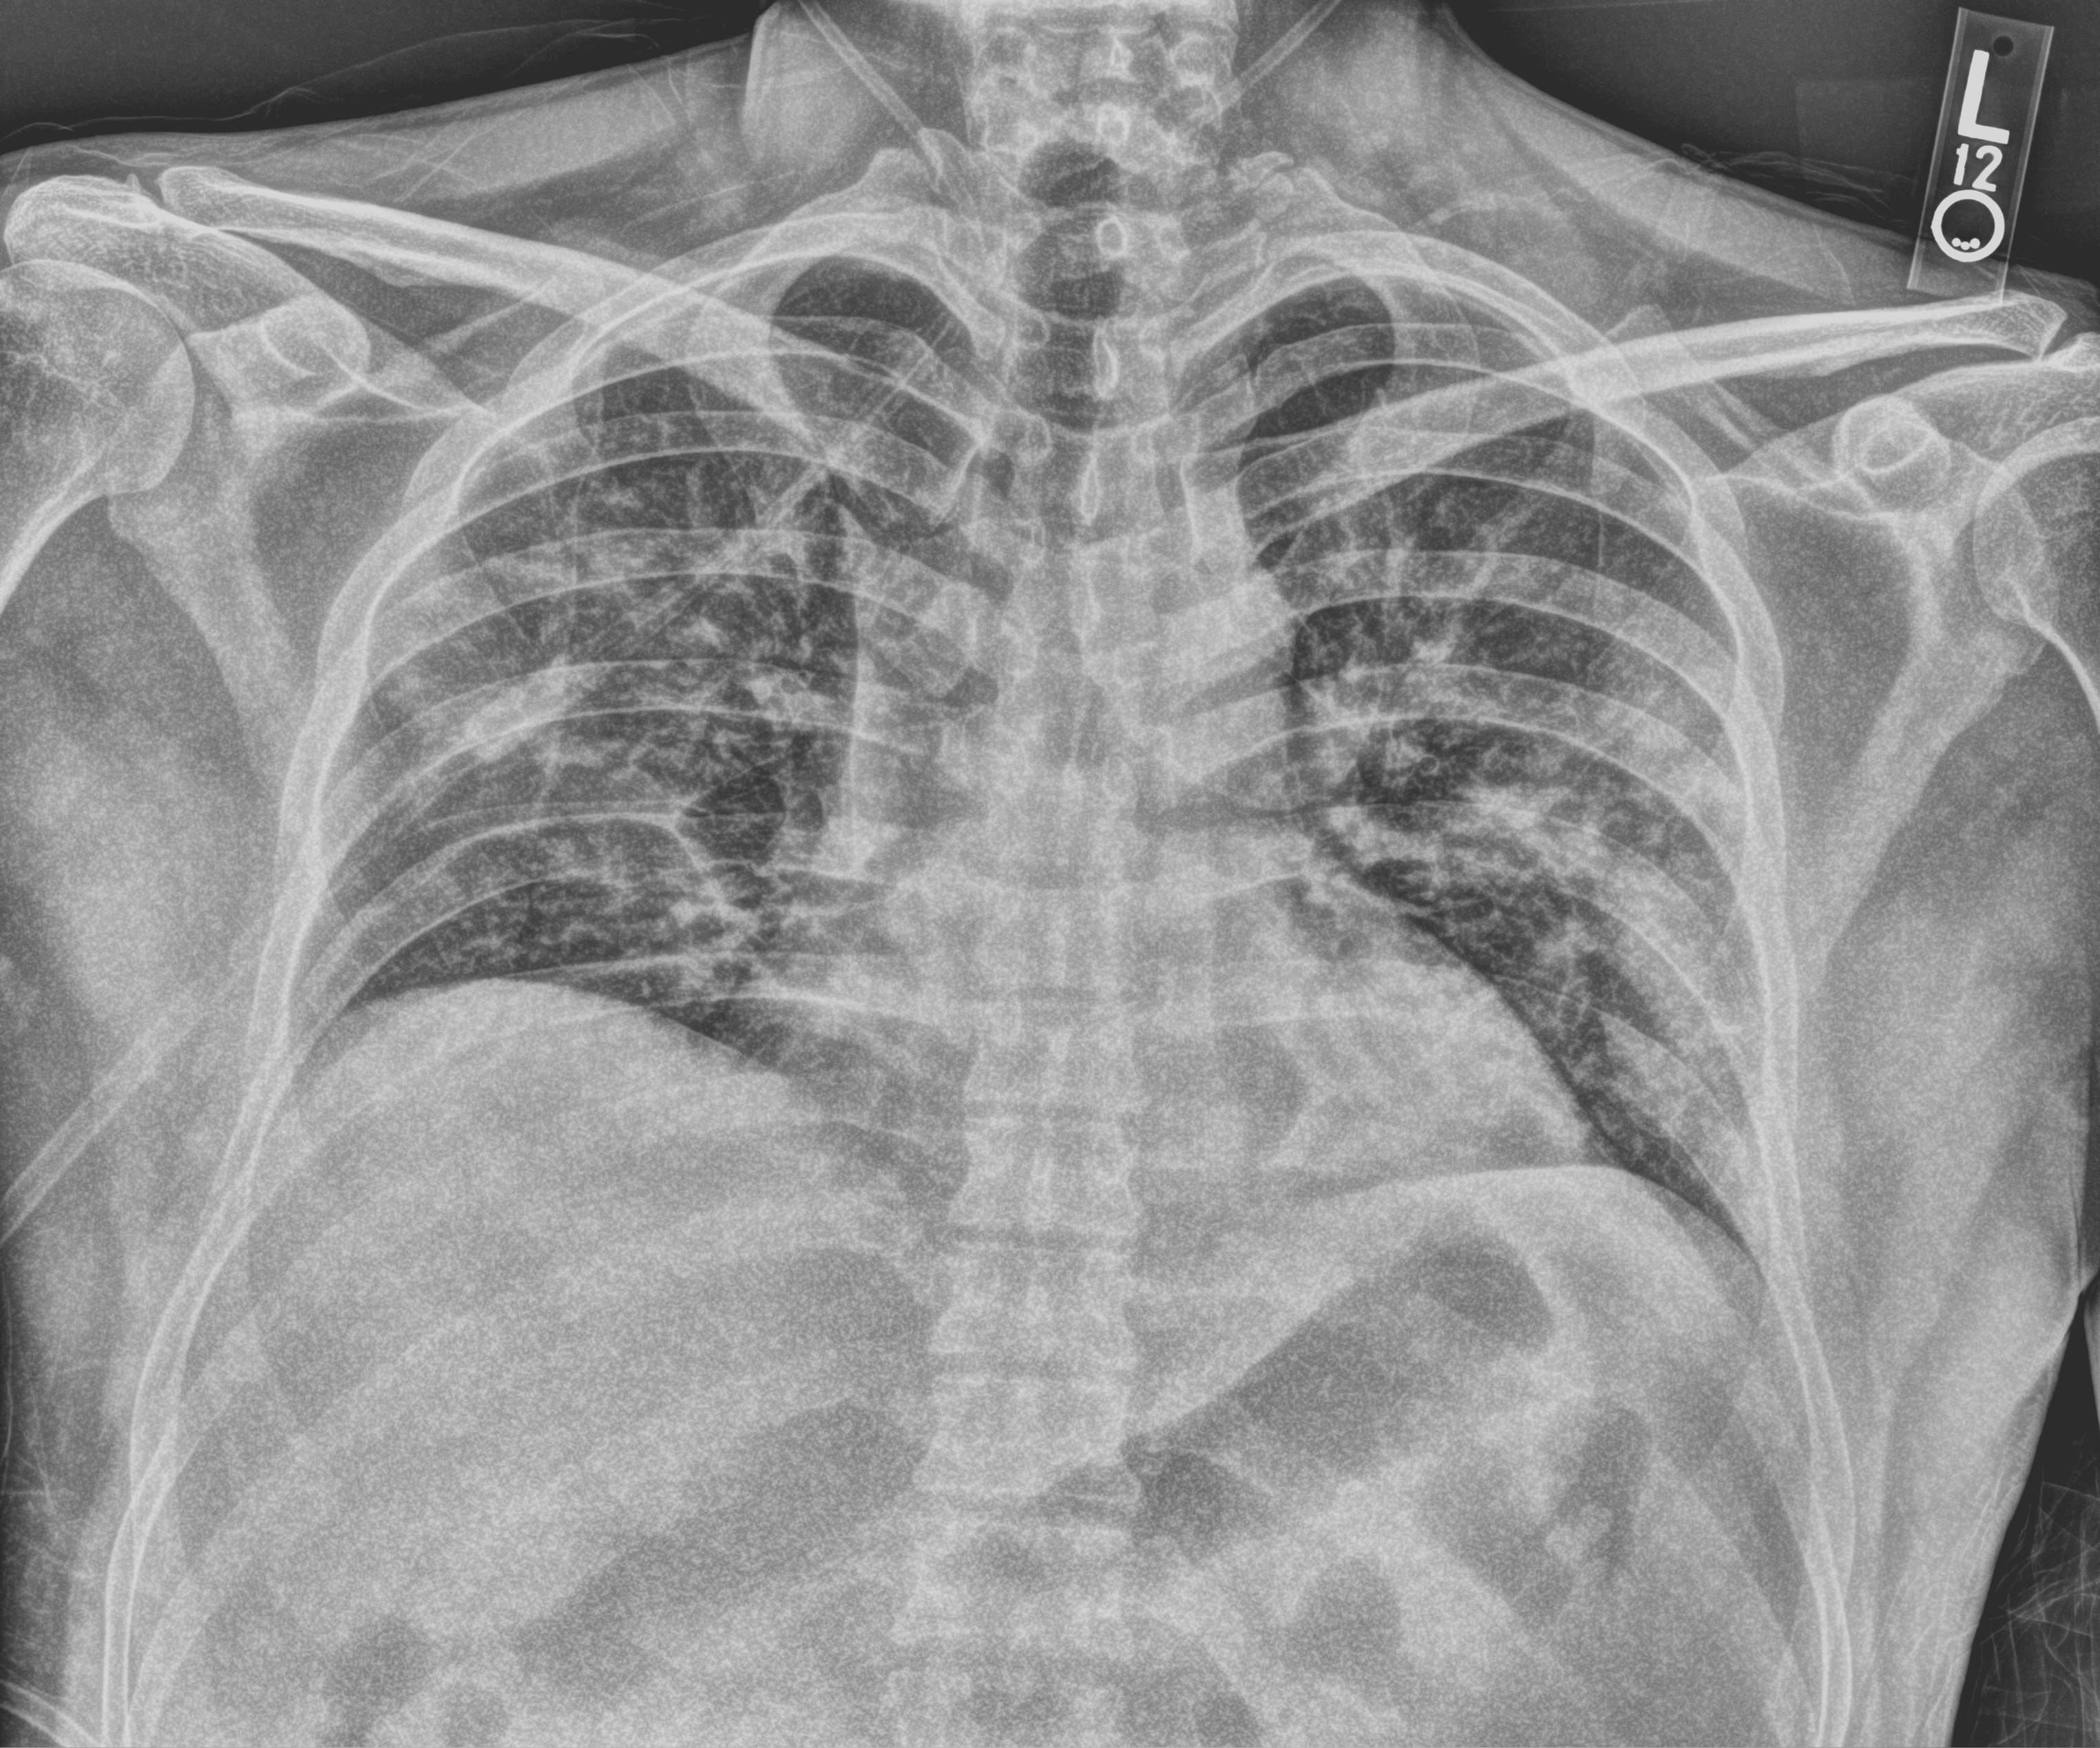
Portable chest radiograph; anteroposterior (AP) projection. Patient hospitalised with COVID-19; male, aged 18–59 years.
Hospital-stay facts (about this admission, not read from this image; timing relative to this image not recorded):
- smoking status (admission record): never
- admitted to intensive care during this hospital stay: no
- mechanically ventilated during this hospital stay: no